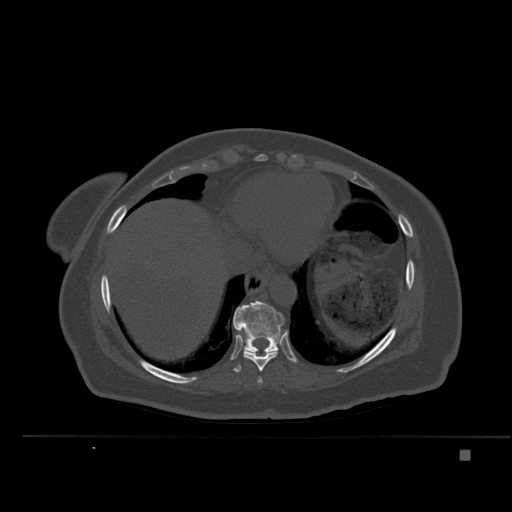
CT including the spine, one axial slice. Position 292 of 477 along the scan axis. Bone window (W 1800 / L 400 HU). 1.5 mm slice thickness. 512 × 512 image matrix, field of view 422 × 422 mm. Patient: female, 74 years. From the clinical record (not read from this slice): primary cancer: colon.
Annotated regions visible in this slice (semi-automatic segmentation, software-assisted and operator-edited):
- T10 vertebra: bounding box (x1, y1, x2, y2) in pixels: (233, 301, 284, 353)
- T8 vertebra: (257, 377, 263, 384)
- T9 vertebra: (233, 311, 281, 373)